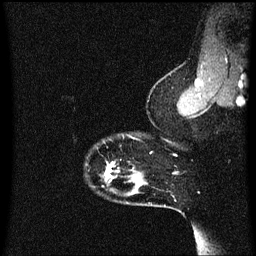
Breast MRI (dynamic contrast-enhanced), one sagittal slice. Position 54 of 60 along the scan axis. Dynamic contrast-enhanced series, image 2 of 3 at this slice position (ordered by acquisition). 1.5 T. TE 4.2 ms, TR 8.4 ms. 2 mm slice thickness. 256 × 256 image matrix. Patient: female, 33 years.
Structures marked on this image (semi-automatically segmented with operator editing):
- analysis volume of interest (the breast-tissue region the enhancement analysis was run in; not a lesion): bounding box (x1, y1, x2, y2) in pixels: (105, 134, 149, 191)
- tumour enhancement mask (voxels above the 70 % enhancement threshold inside the analysis volume of interest): (106, 162, 116, 179)